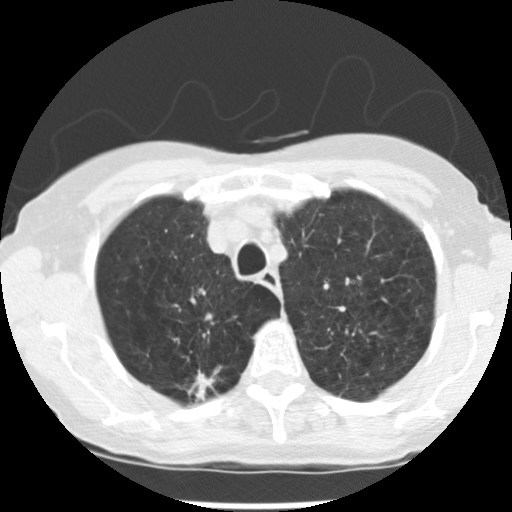
Low-dose screening chest CT, axial slice; first (baseline) screen; lung window (W 1500 / L -600 HU); standard (soft-tissue) reconstruction kernel (STANDARD); 120 kVp; slice 47 of 265 in the series. Female participant, aged 72 years at enrolment. Current smoker at enrolment.
Lesion marked by an expert reader, box from (x=183, y=363) to (x=233, y=406) px. The screening reader recorded 3 non-calcified nodules or masses ≥4 mm on this exam; which of them this box marks is not recorded. Later outcome: lung cancer diagnosed 50 days after this screen — adenocarcinoma, NOS, right upper lobe, moderately differentiated (G2), stage IB (AJCC 6th edition), 22 mm at pathology.